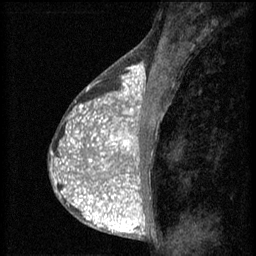
Breast MRI (dynamic contrast-enhanced), one sagittal slice. 3 images stored at this slice position (order not interpretable as contrast timing). 1.5 T. TE 4.2 ms, TR 8.2 ms. 2 mm slice thickness. 256 × 256 image matrix, field of view 180 × 180 mm. Patient: female, 38 years.
Annotated regions visible in this slice (semi-automatically segmented with operator editing):
- analysis volume of interest (the breast-tissue region the enhancement analysis was run in; not a lesion): bounding box [x1, y1, x2, y2] px = [92, 112, 152, 171]
- tumour enhancement mask (voxels above the 70 % enhancement threshold inside the analysis volume of interest): [92, 112, 141, 171]